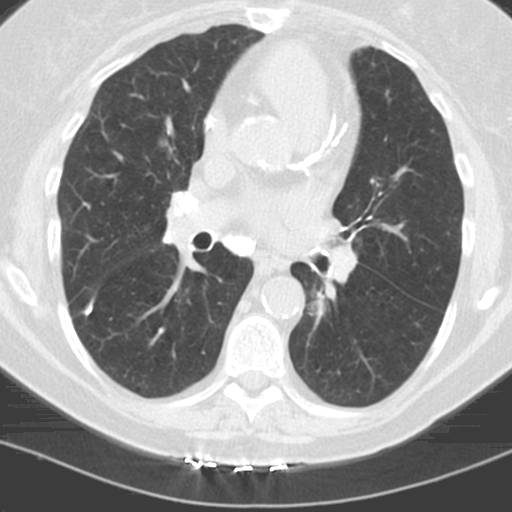
Low-dose screening chest CT, axial slice; first (baseline) screen; lung window (W 1500 / L -600 HU); 3.2 mm slice thickness; slice 63 of 121 in the series. Female participant, aged 60 years at enrolment. Former smoker at enrolment.
Expert reader's lesion annotation, bounding box (x1, y1, x2, y2) in pixels: (293, 281, 341, 333). The screening reader recorded 3 non-calcified nodules or masses ≥4 mm on this exam; which of them this box marks is not recorded. Official screen result: positive, change unspecified: nodule(s) >= 4 mm or enlarging nodule(s), mass(es), or other non-specific abnormalities suspicious for lung cancer.